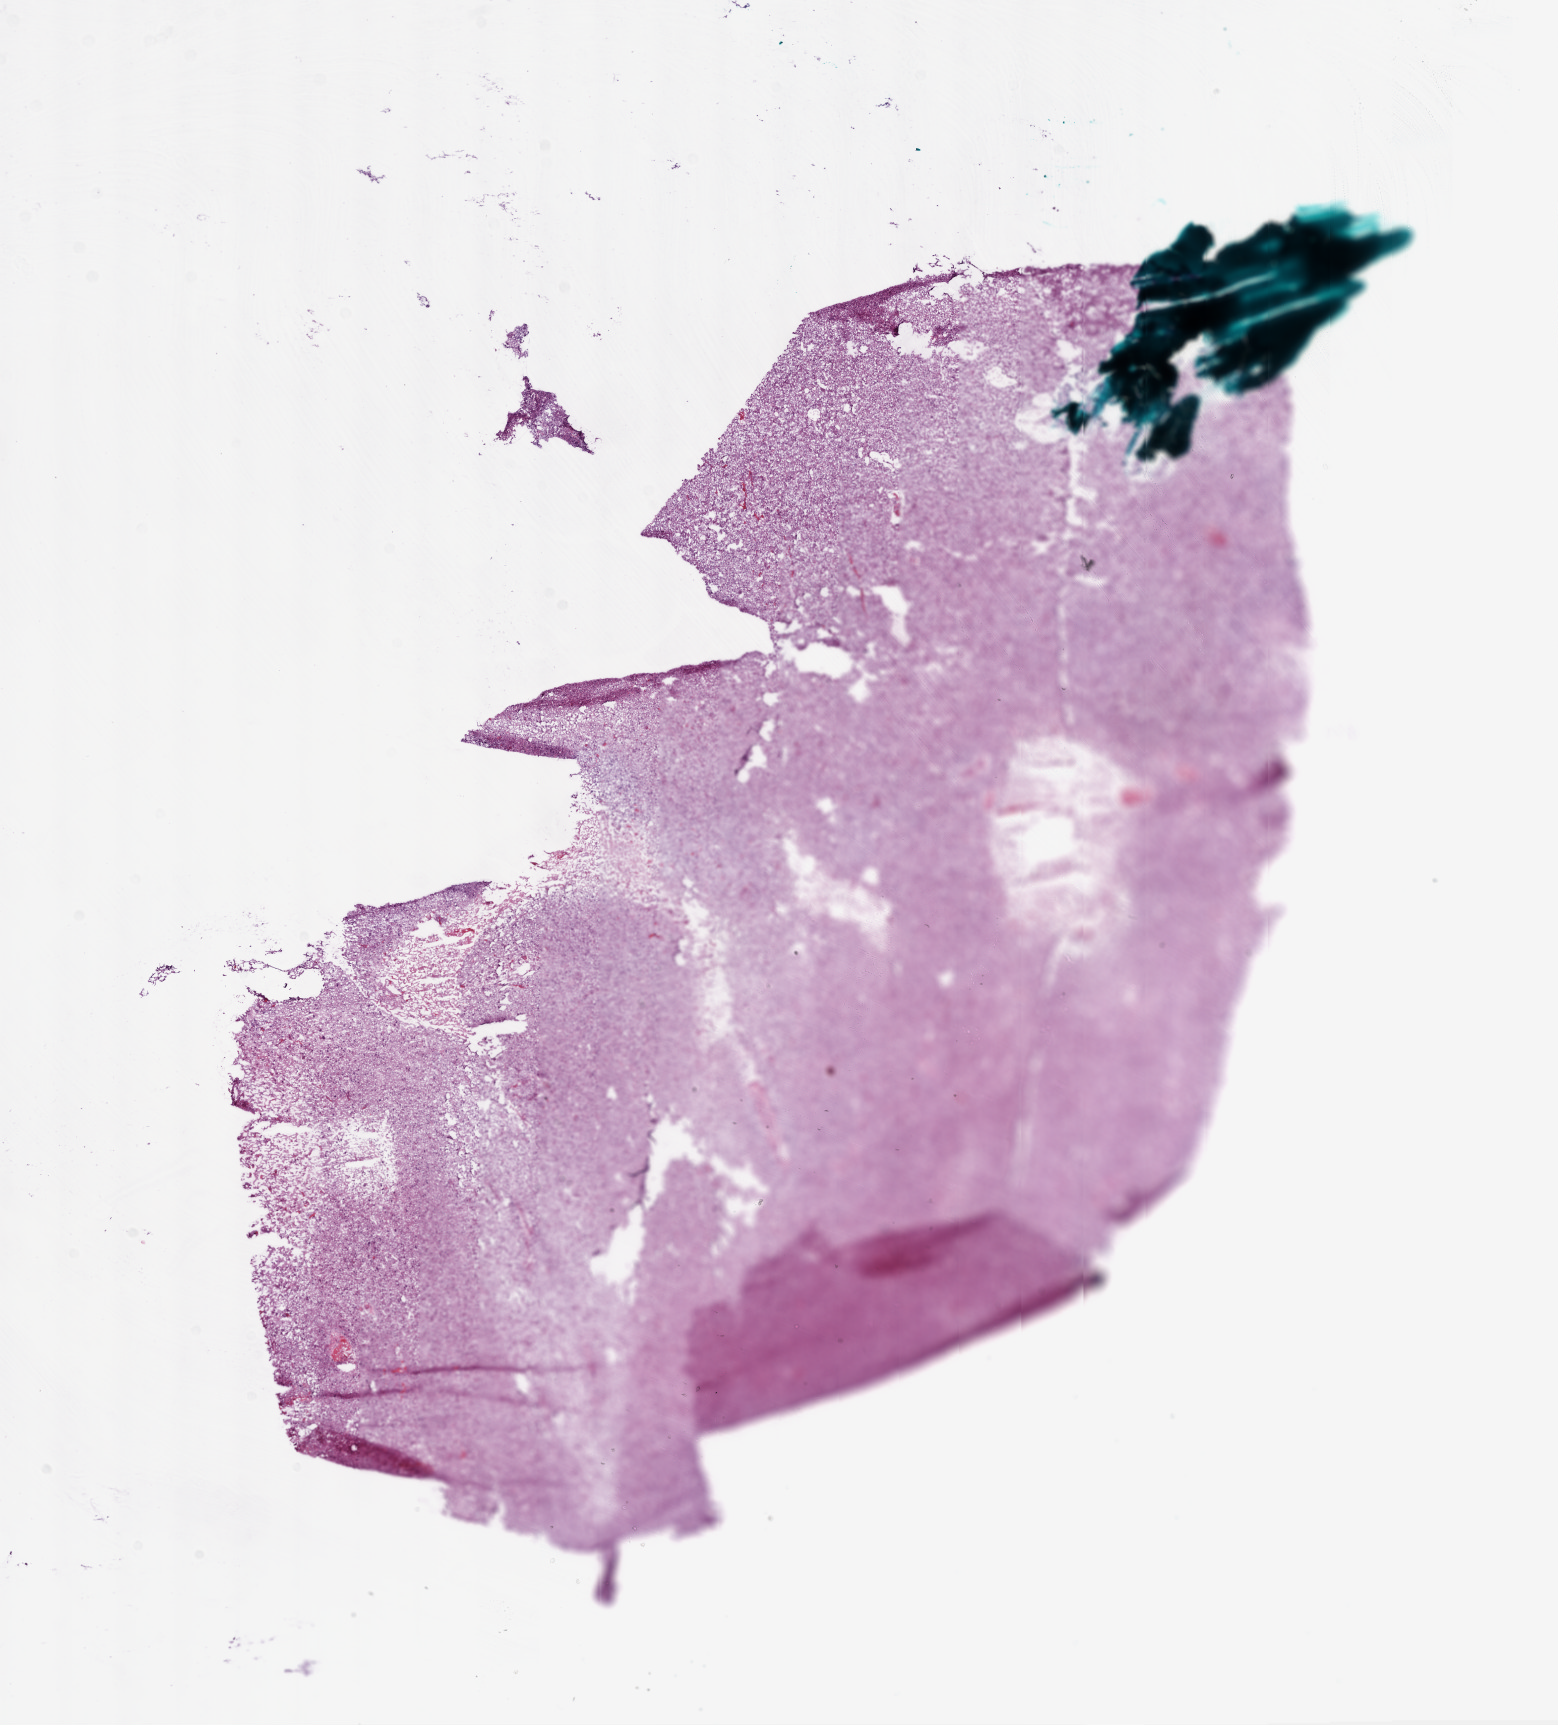
Digitized H&E tissue section (whole slide), whole scanned area (about 12.6 x 13.9 mm) shown as a low-resolution overview; frozen section; primary tumour sample from the brain. Patient: male, age at initial diagnosis 71 years. Pathologist review of this section (percent, as recorded): tumour cells 95%, tumour nuclei 90%, normal cells 0%, stromal cells 0%, necrosis 5%.
- pathologic diagnosis: Glioblastoma